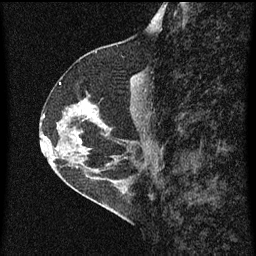
Breast MRI (dynamic contrast-enhanced), one sagittal slice. Position 29 of 60 along the scan axis. Dynamic contrast-enhanced series, image 2 of 3 at this slice position (ordered by acquisition). 1.5 T. TE 4.2 ms, TR 8 ms. 256 × 256 image matrix. Patient: female, 56 years.
Outlined on this slice (semi-automatic segmentation, software-assisted and operator-edited):
- analysis volume of interest (the breast-tissue region the enhancement analysis was run in; not a lesion): bounding box (x1, y1, x2, y2) in pixels: (49, 96, 110, 159)
- tumour enhancement mask (voxels above the 70 % enhancement threshold inside the analysis volume of interest): (78, 112, 98, 143)